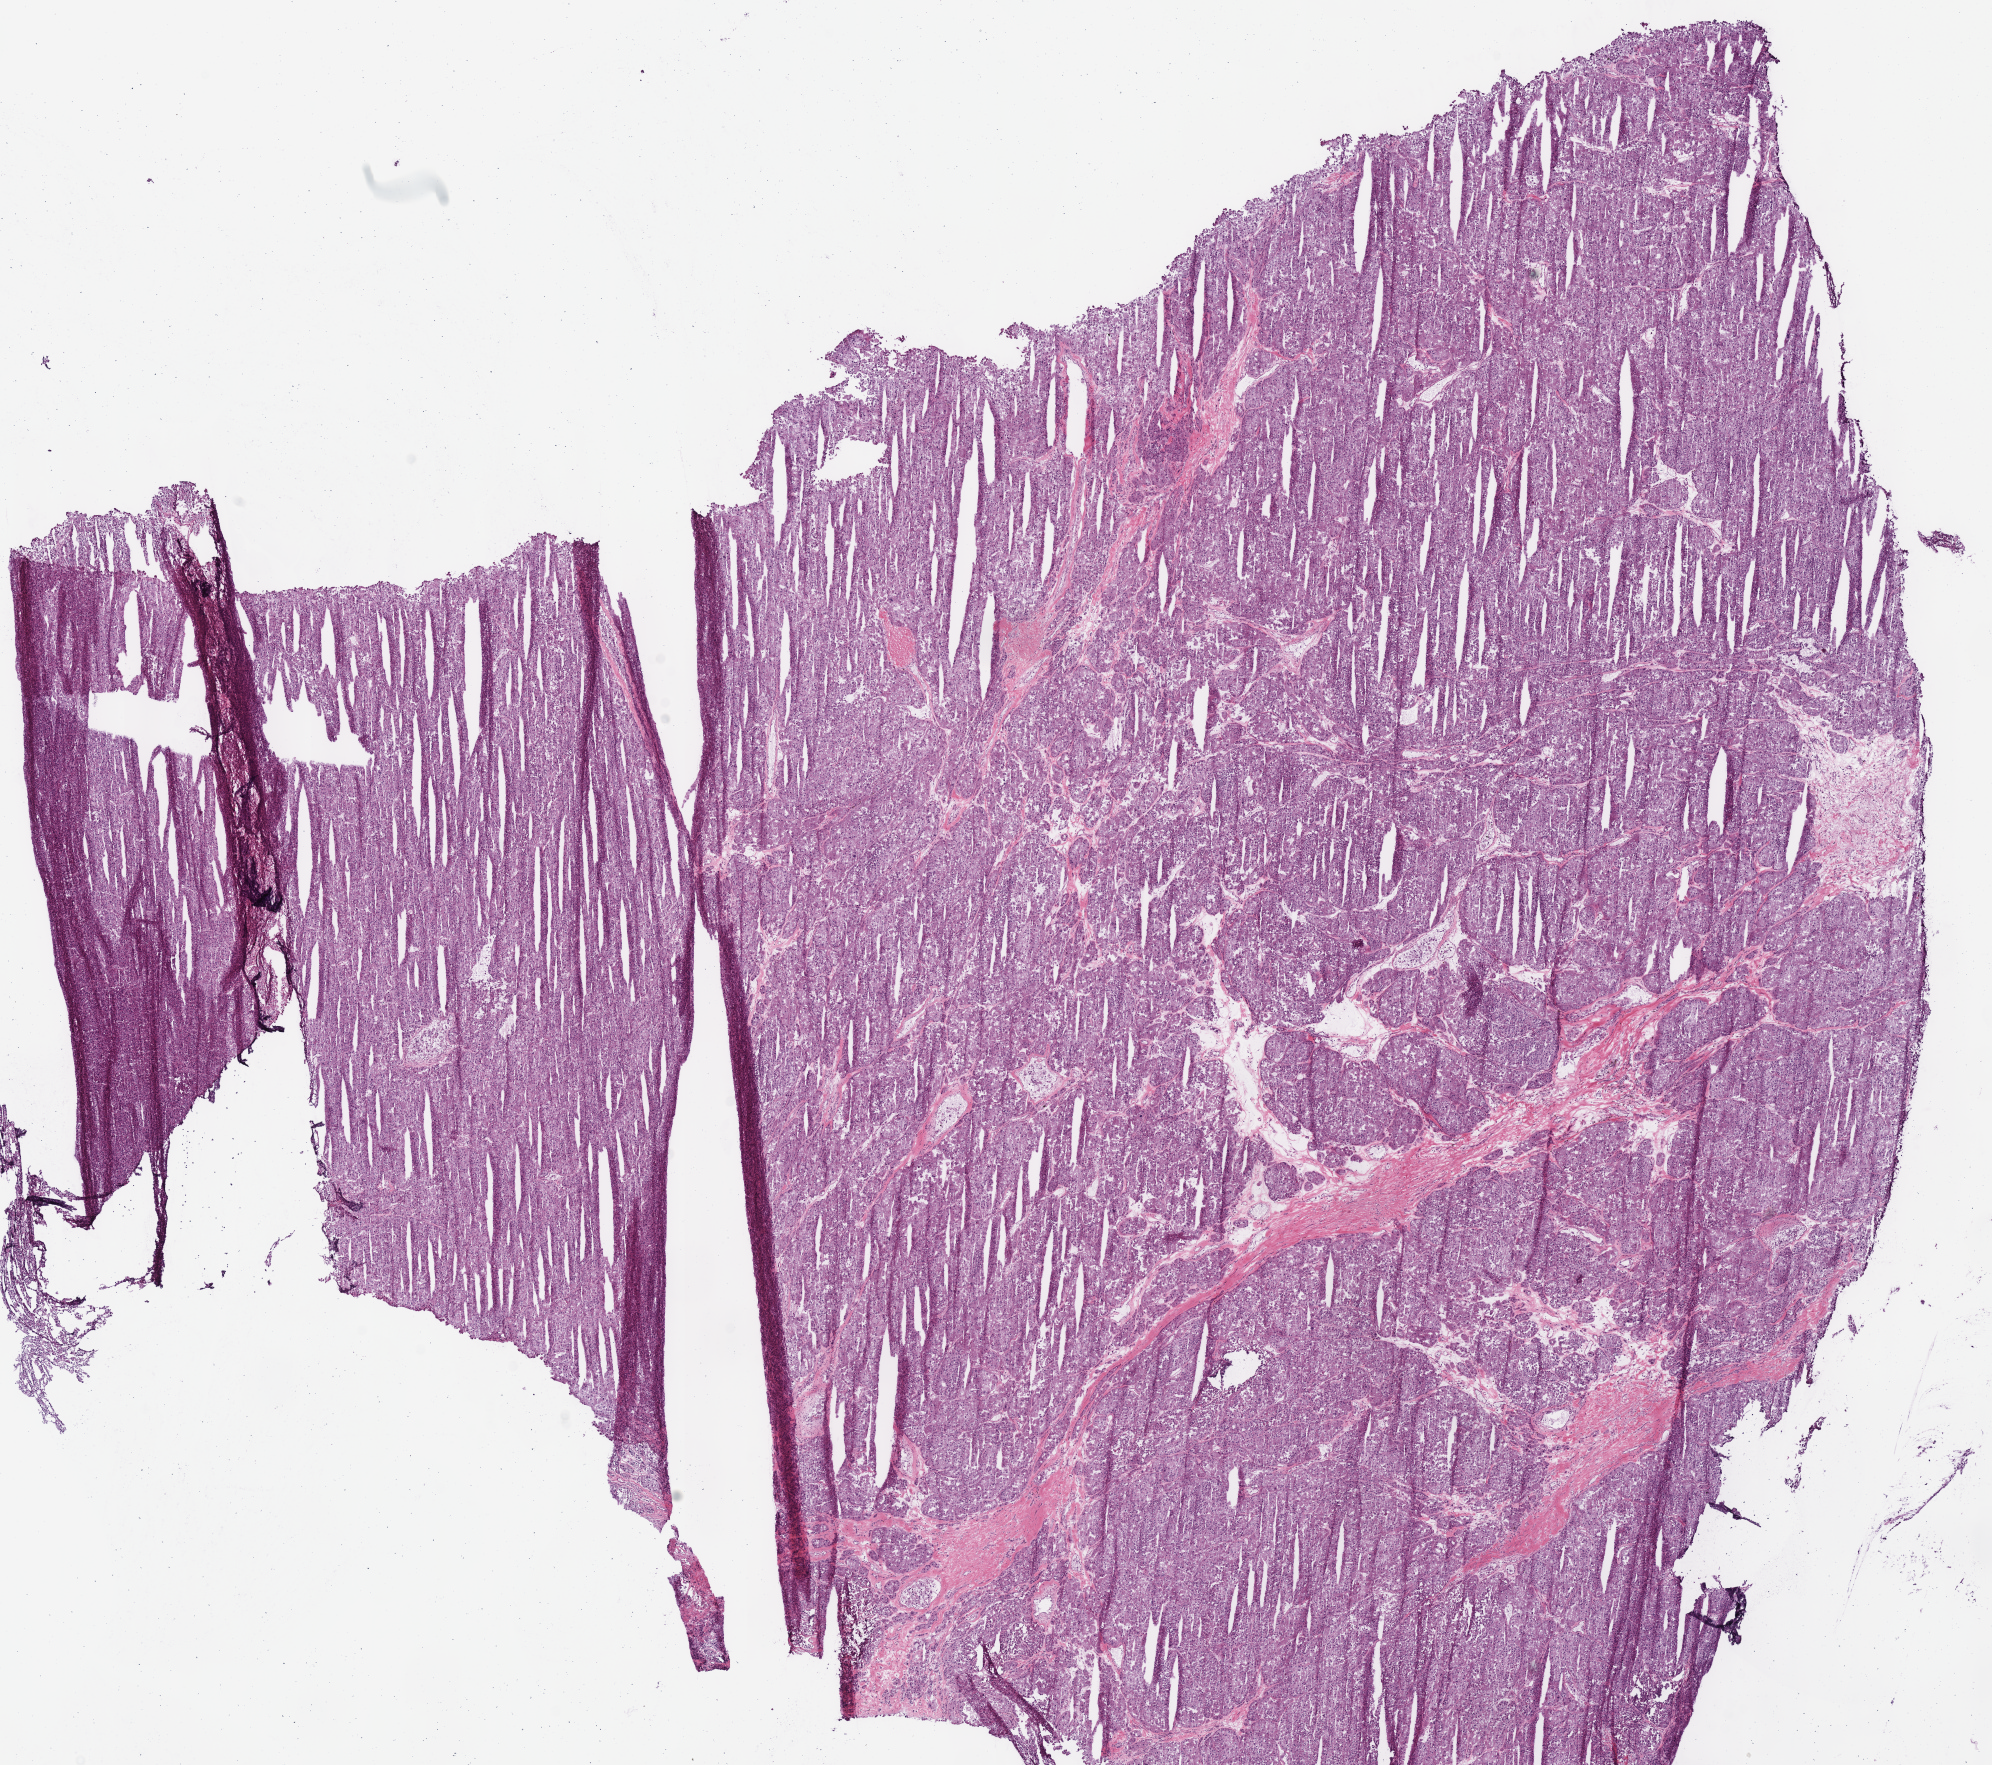
Whole-slide histology image, H&E — low-resolution overview of the scanned area, about 15.7 x 13.9 mm (slide scanned at 40x), frozen section from the bottom of the tissue portion, kidney, primary tumour sample. Male, age 67 years at initial diagnosis. Pathologist review of this section (percent, as recorded): tumour cells 90%, tumour nuclei 90%, normal cells 0%, stromal cells 10%, necrosis 0%.
TNM: T3a N1 M1. Laterality: left. Lymph nodes positive (case pathology): 1 of 33 examined. AJCC pathologic stage: IV (6th edition). Histologic diagnosis: Renal cell carcinoma, chromophobe type.